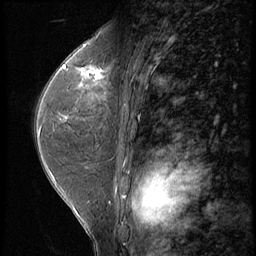
Breast MRI (dynamic contrast-enhanced), one sagittal slice. Slice 34 of 56 in the series (ordered by position). 3 images stored at this slice position (order not interpretable as contrast timing). 1.5 T. TE 4.2 ms, TR 9 ms. 256 × 256 image matrix, field of view 180 × 180 mm. Patient: female, 44 years. From the clinical record (not read from this slice): setting: breast cancer imaged before/during neoadjuvant chemotherapy; receptor status: triple-negative.
Outlined on this slice (semi-automatic segmentation, software-assisted and operator-edited):
- analysis volume of interest (the breast-tissue region the enhancement analysis was run in; not a lesion): bounding box (x1, y1, x2, y2) in pixels: (71, 54, 112, 99)
- tumour enhancement mask (voxels above the 140 % enhancement threshold inside the analysis volume of interest): (77, 67, 104, 79)